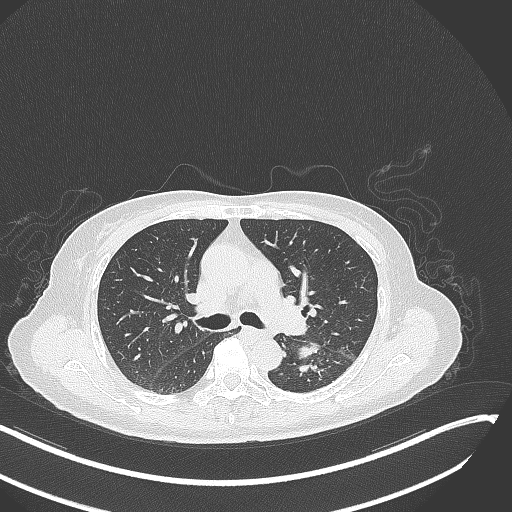
Chest CT, one axial slice; position 178 of 342 along the scan axis; reconstruction kernel B70f; 120 kVp; lung window (W 1500 / L -600 HU); 512 × 512 image matrix. Female patient, age 64 years. Case-level facts recorded for this patient, not image findings: clinical TNM (as recorded): T3 N1 M1; histopathological grade: G3.
Structures marked on this image (bounding box drawn by a radiologist):
- lung tumour (recorded histology: small cell carcinoma): bounding box <296,335,320,360> (left, top, right, bottom; pixels)